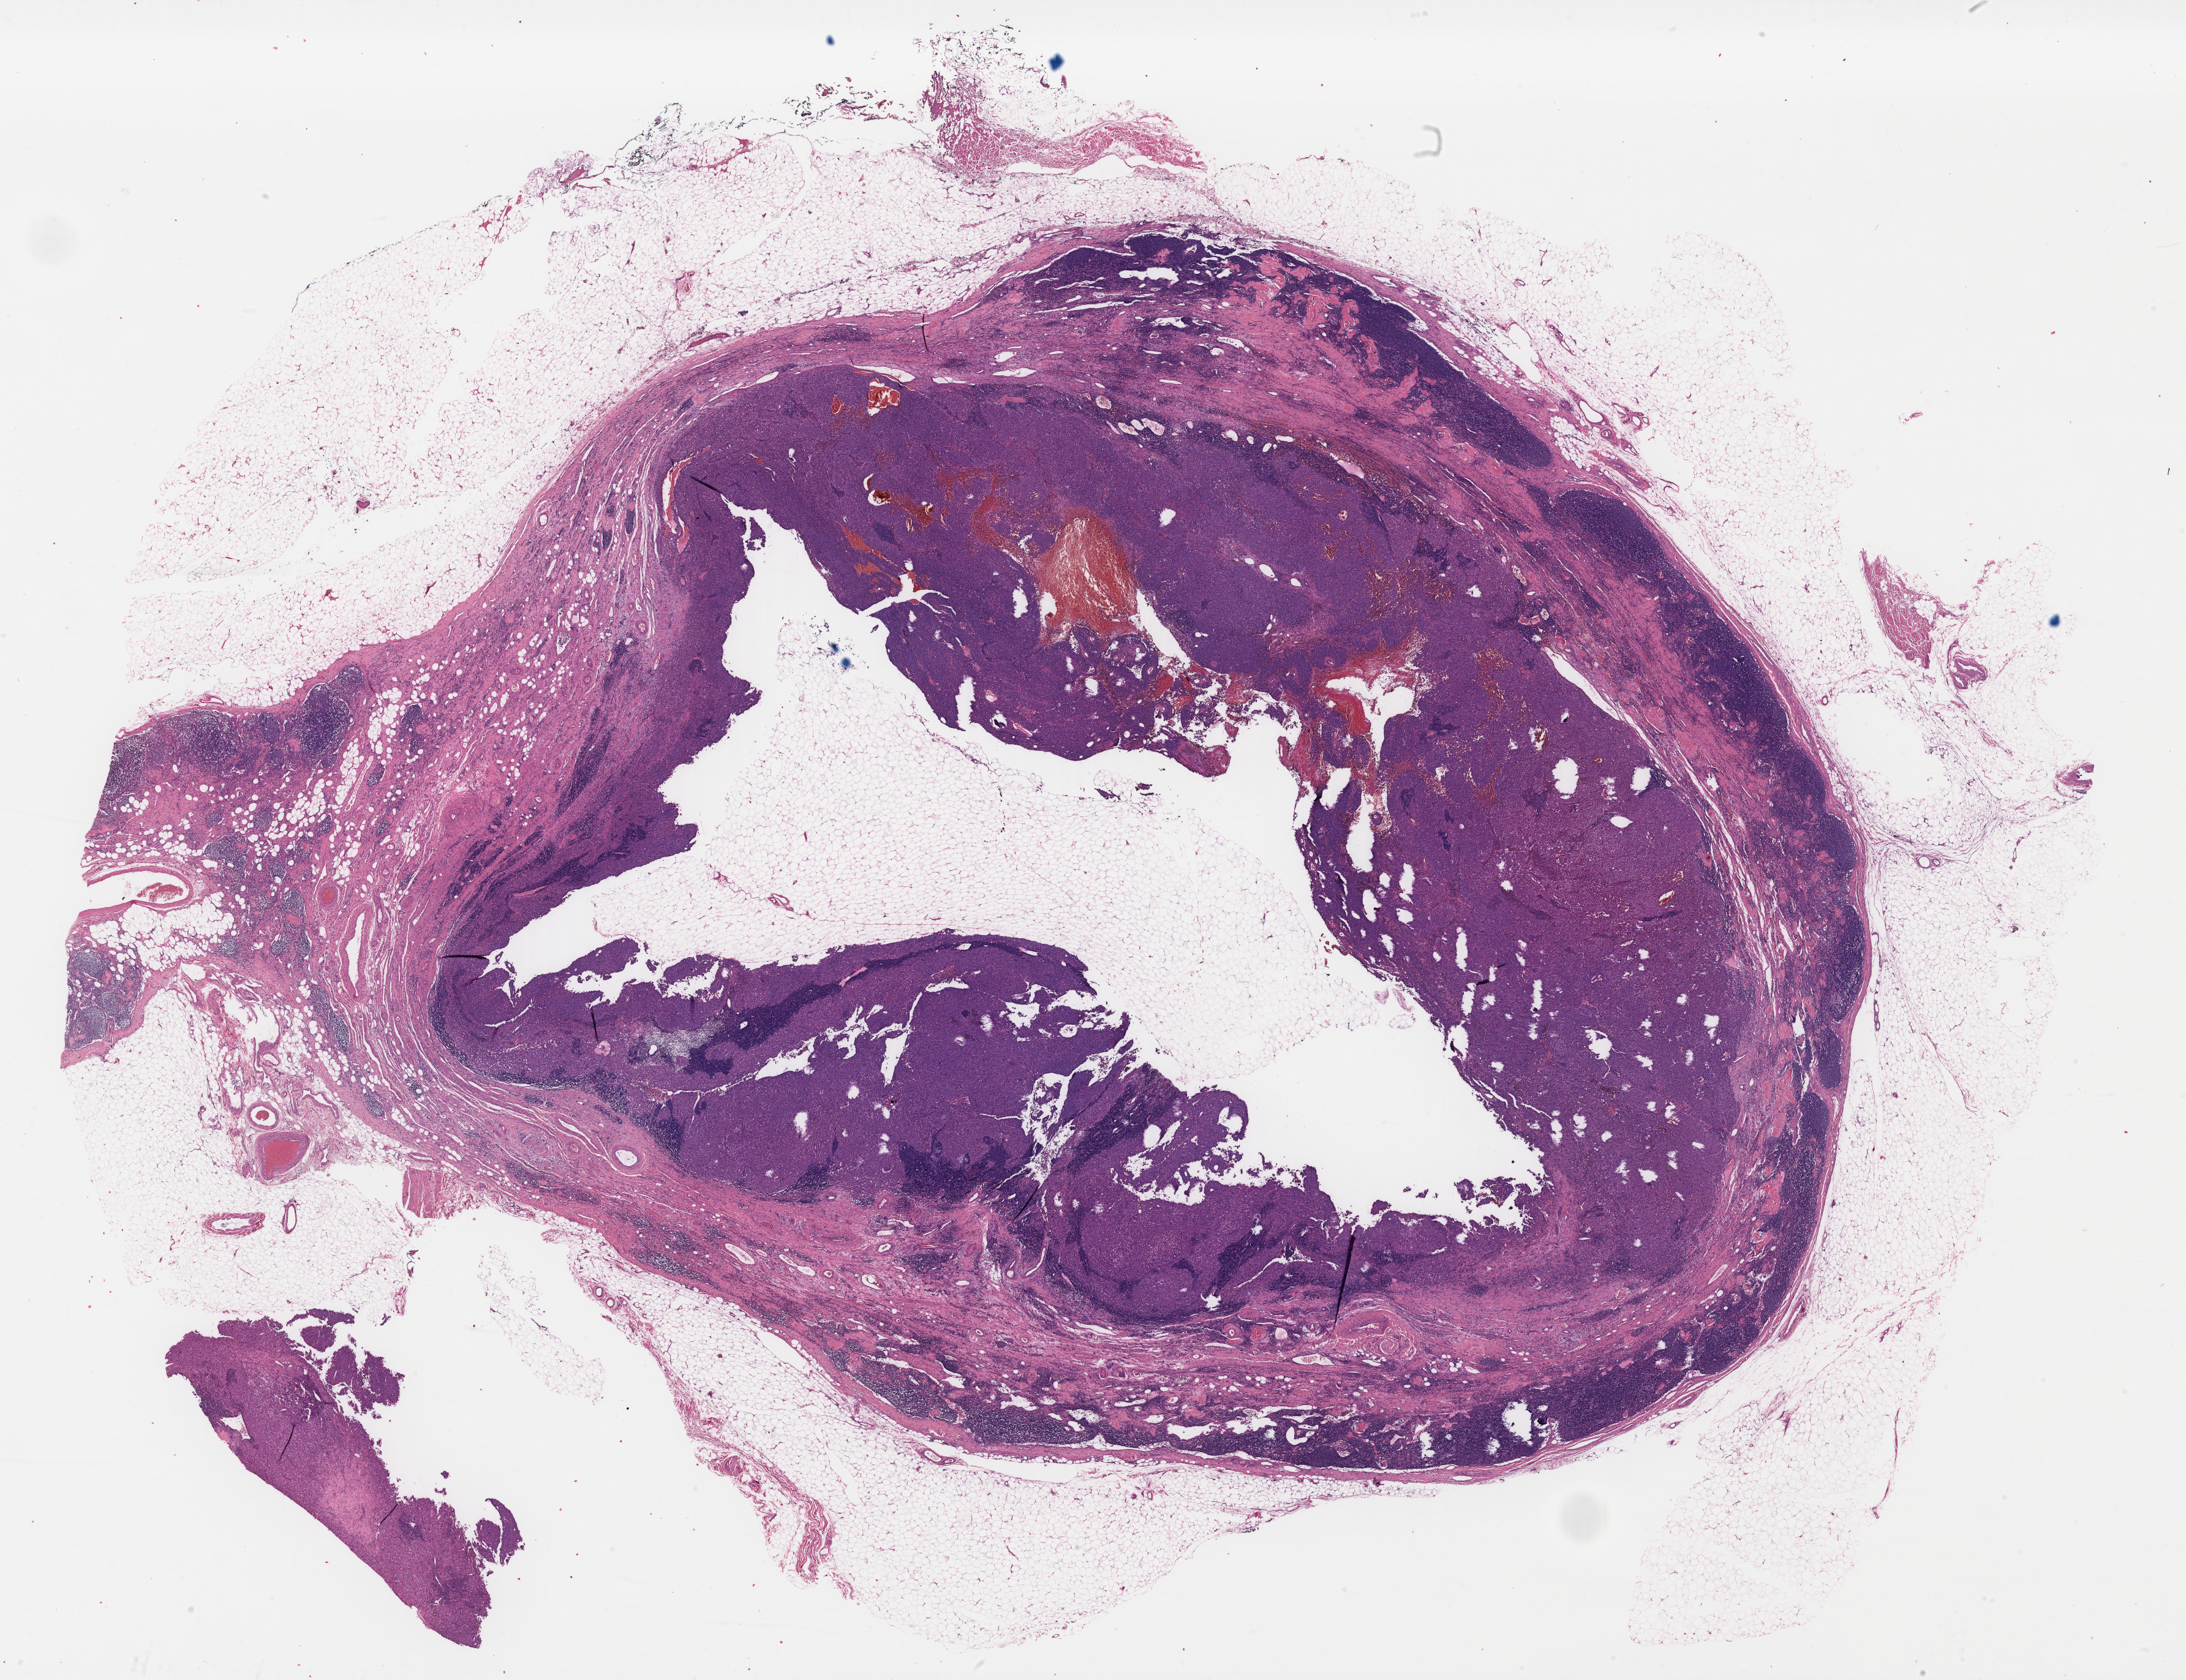
Digitized H&E tissue section (whole slide) — low-resolution overview of the scanned area, about 28.3 x 21.8 mm (acquisition: 40x scan), formalin-fixed paraffin-embedded (FFPE) diagnostic section, sample: primary tumour, skin. Male patient.
Diagnosis: Malignant melanoma, NOS.